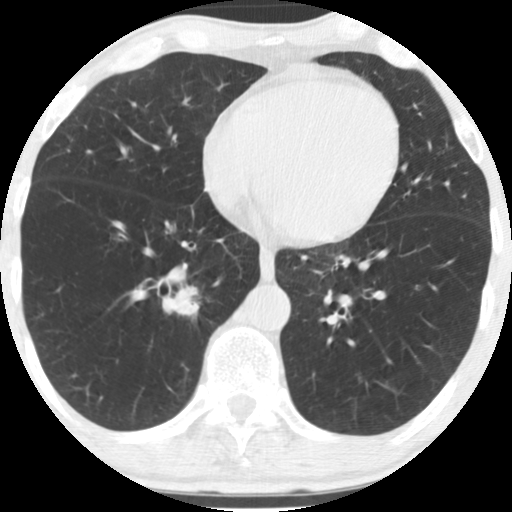
Low-dose screening chest CT, one axial slice; position 57 of 170 along the scan axis; 120 kVp; lung window (W 1500 / L -600 HU); 2.5 mm slice thickness; 512 × 512 image matrix.
Annotated regions visible in this slice (expert manual segmentation):
- lesion 1 (tumor, lower lobe of right lung): box from (x=173, y=286) to (x=199, y=315) px